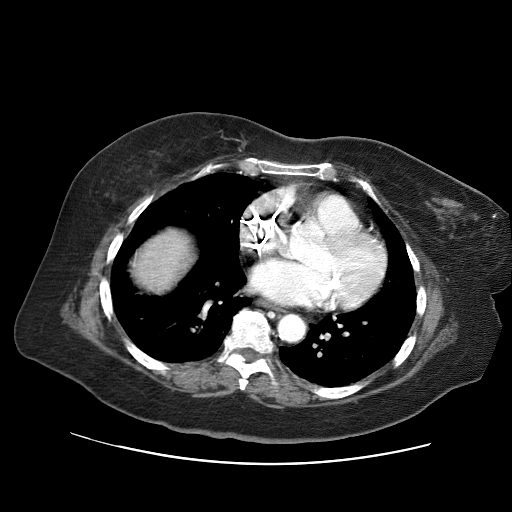
Contrast-enhanced abdominal CT (liver protocol), one axial slice; slice 66 of 71 in the series (ordered by position); reconstruction kernel STANDARD; soft-tissue window (W 400 / L 40 HU); 512 × 512 image matrix, field of view 400 × 400 mm. Case-level facts recorded for this patient, not image findings: diagnosis: hepatocellular carcinoma (patient treated with transarterial chemoembolisation; whether this scan precedes or follows treatment is not stated here); TNM stage (as recorded): Stage-II; Child-Pugh class: A.
Structures marked on this image (semi-automatic segmentation, software-assisted and operator-edited):
- abdominal aorta: bounding box [x1, y1, x2, y2] px = [278, 316, 303, 339]
- liver parenchyma outside the tumour (the mass and vessels are separate outlines, so this box may not span the whole liver): [135, 230, 188, 288]